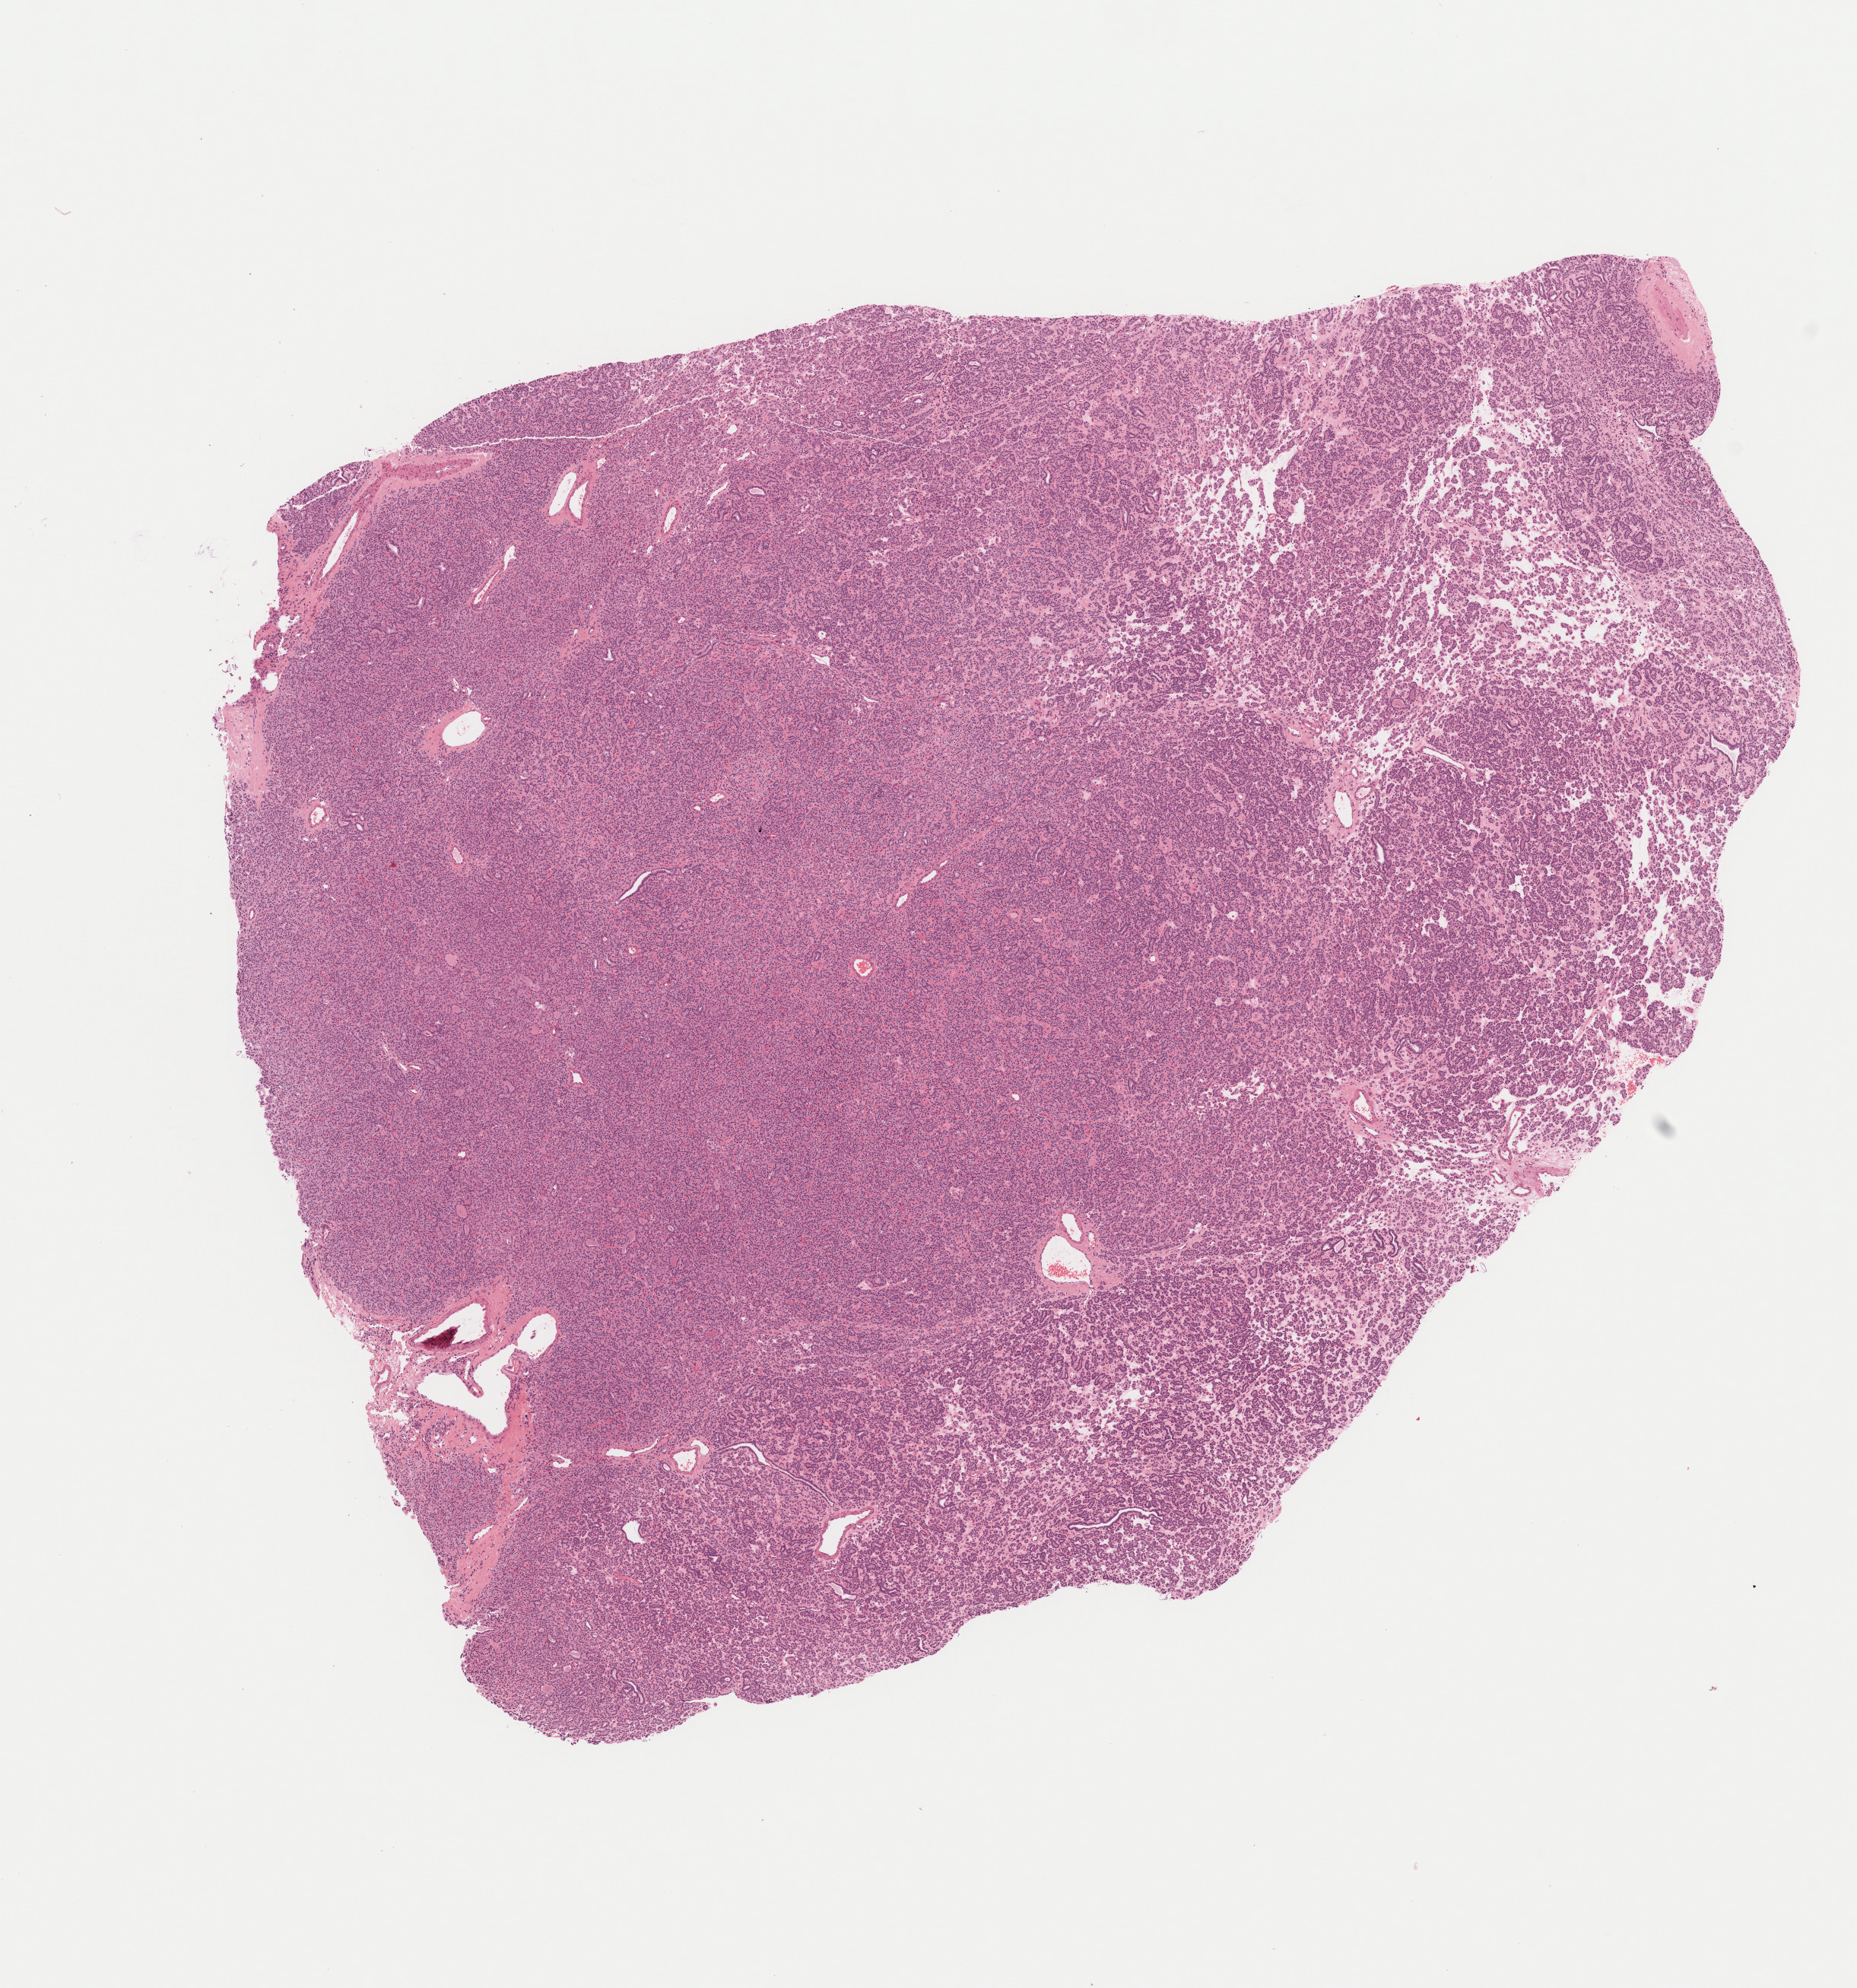
Whole-slide histology image, H&E-stained — a low-resolution overview of the entire scanned area, about 9.8 x 10.5 mm (acquisition: 40x scan). Formalin-fixed paraffin-embedded (FFPE) diagnostic section. Primary tumour sample from the thyroid. Female patient; age at initial diagnosis 49 years.
Pathologic diagnosis: Papillary adenocarcinoma, NOS (thyroid gland).